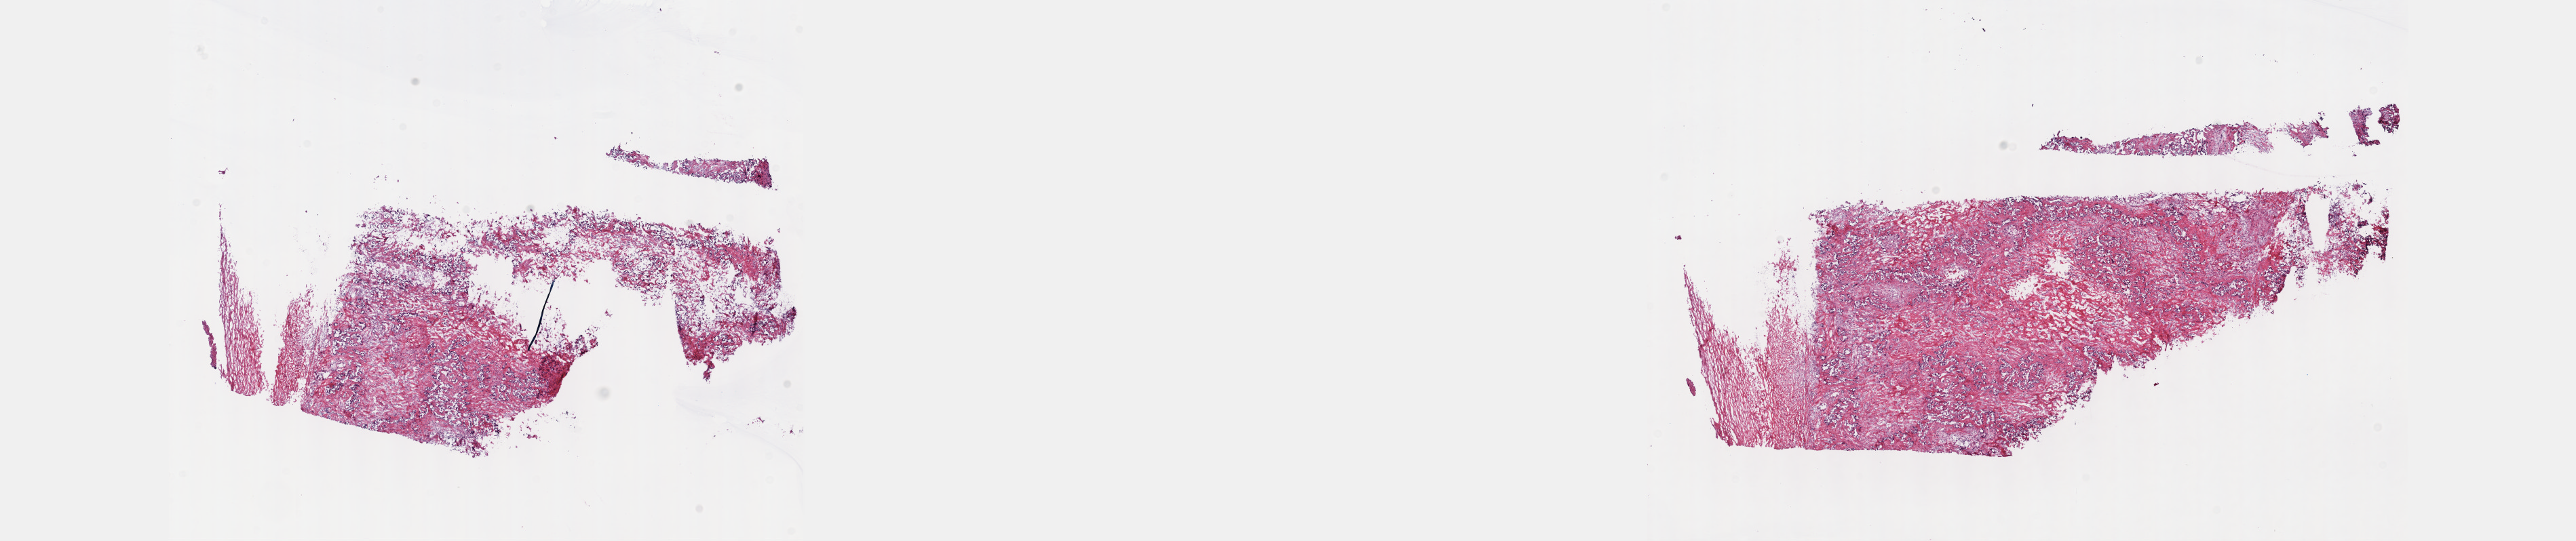
Whole-slide histology image, H&E-stained, whole scanned area (about 30.7 x 6.4 mm, acquisition: 40x scan) shown as a low-resolution overview, frozen section from the top of the tissue portion, bile duct, primary tumour sample. Patient: female, age at initial diagnosis 29 years. Histologic grade: G3 (poorly differentiated). Composition of this section per pathologist review: tumour cells 23%, tumour nuclei 85%, normal cells 0%, stromal cells 75%, necrosis 2%. Infiltration values recorded for this section: lymphocyte infiltration 4%, monocyte infiltration 0%, neutrophil infiltration 0%.
AJCC pathologic stage: II (7th edition). Diagnosis: Cholangiocarcinoma (intrahepatic bile duct).